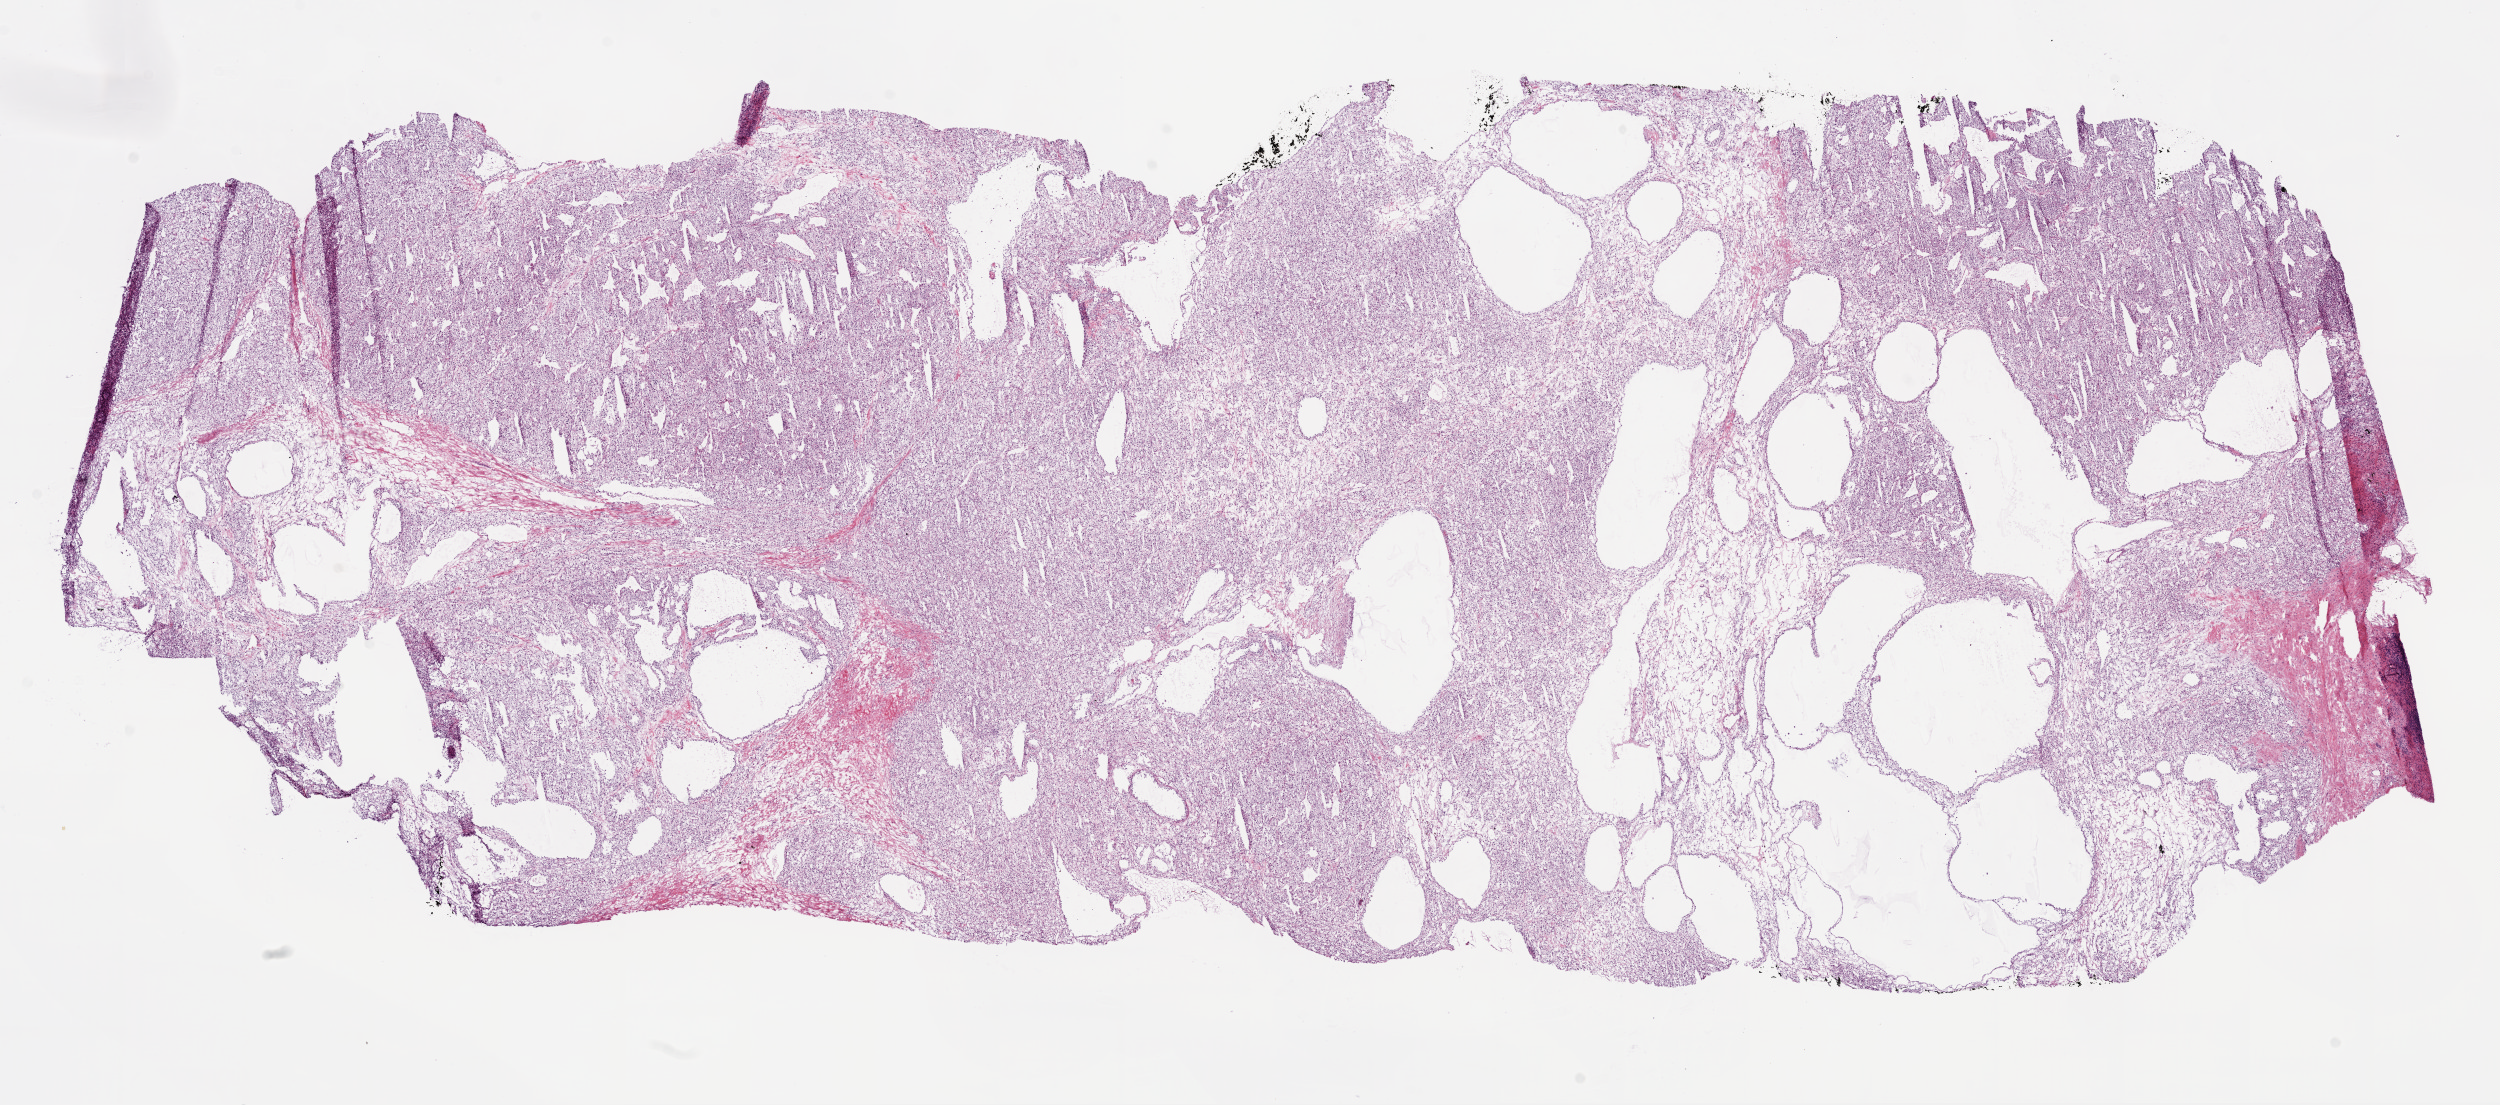
H&E whole-slide image — whole scanned area (about 20.1 x 8.9 mm, slide scanned at 20x) shown as a low-resolution overview, frozen section from the bottom of the tissue portion, sample: primary tumour, kidney. Patient: male, age at initial diagnosis 51 years. Histologic grade: G2 (moderately differentiated). Slide review estimates, as recorded: tumour cells 90%, tumour nuclei 85%, normal cells 0%, stromal cells 10%, necrosis 0%.
• AJCC pathologic stage: I
• laterality: left
• diagnosis: Clear cell adenocarcinoma, NOS